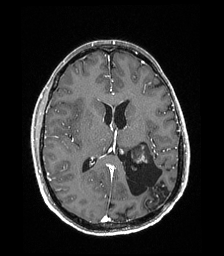
Brain MRI from a brain-tumour surgery series, one axial slice. Slice 89 of 192 in the series (ordered by position). T1-weighted post-contrast. 1 mm slice thickness. 224 × 256 image matrix, field of view 224 × 256 mm. From the clinical record (not read from this slice): histopathology: Low grade glioma; IDH mutation: no; tumour location: Left Parieto-Occipital Intraventricular.
Structures marked on this image (manually delineated by an expert):
- previous resection cavity: bounding box [x1, y1, x2, y2] px = [125, 152, 164, 204]
- tumour: [131, 143, 150, 171]